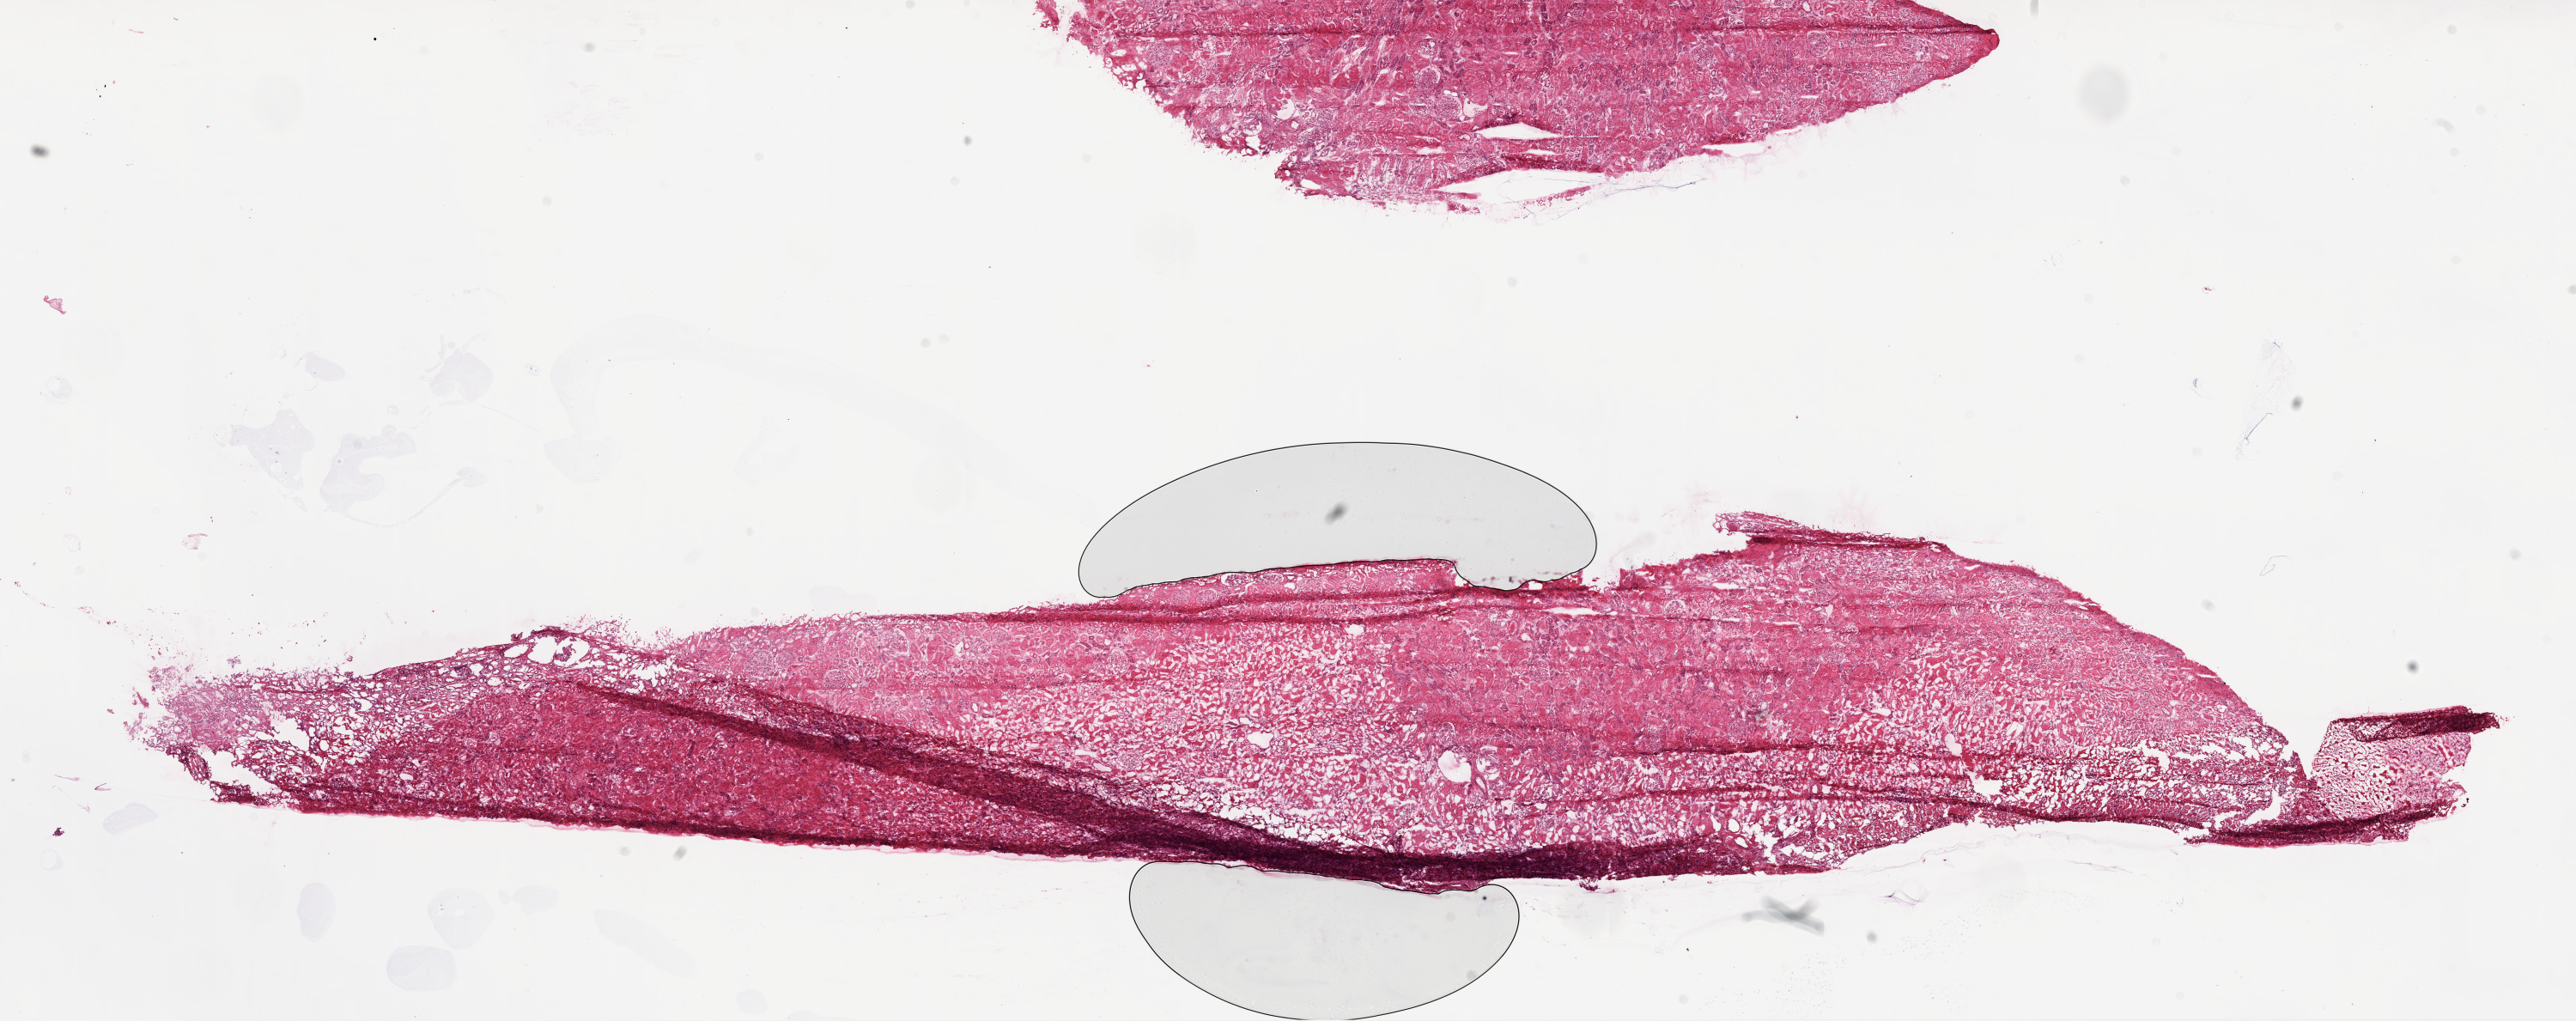
Digitized H&E-stained tissue section (whole slide) — a low-resolution overview of the entire scanned area, about 24.1 x 9.5 mm (slide scanned at 20x), frozen section, sample: solid tissue normal (non-tumour tissue), kidney. Female patient; age at initial diagnosis 39 years.
This section: solid tissue normal sample (biorepository sample class). Patient diagnosis: Clear cell adenocarcinoma, NOS.